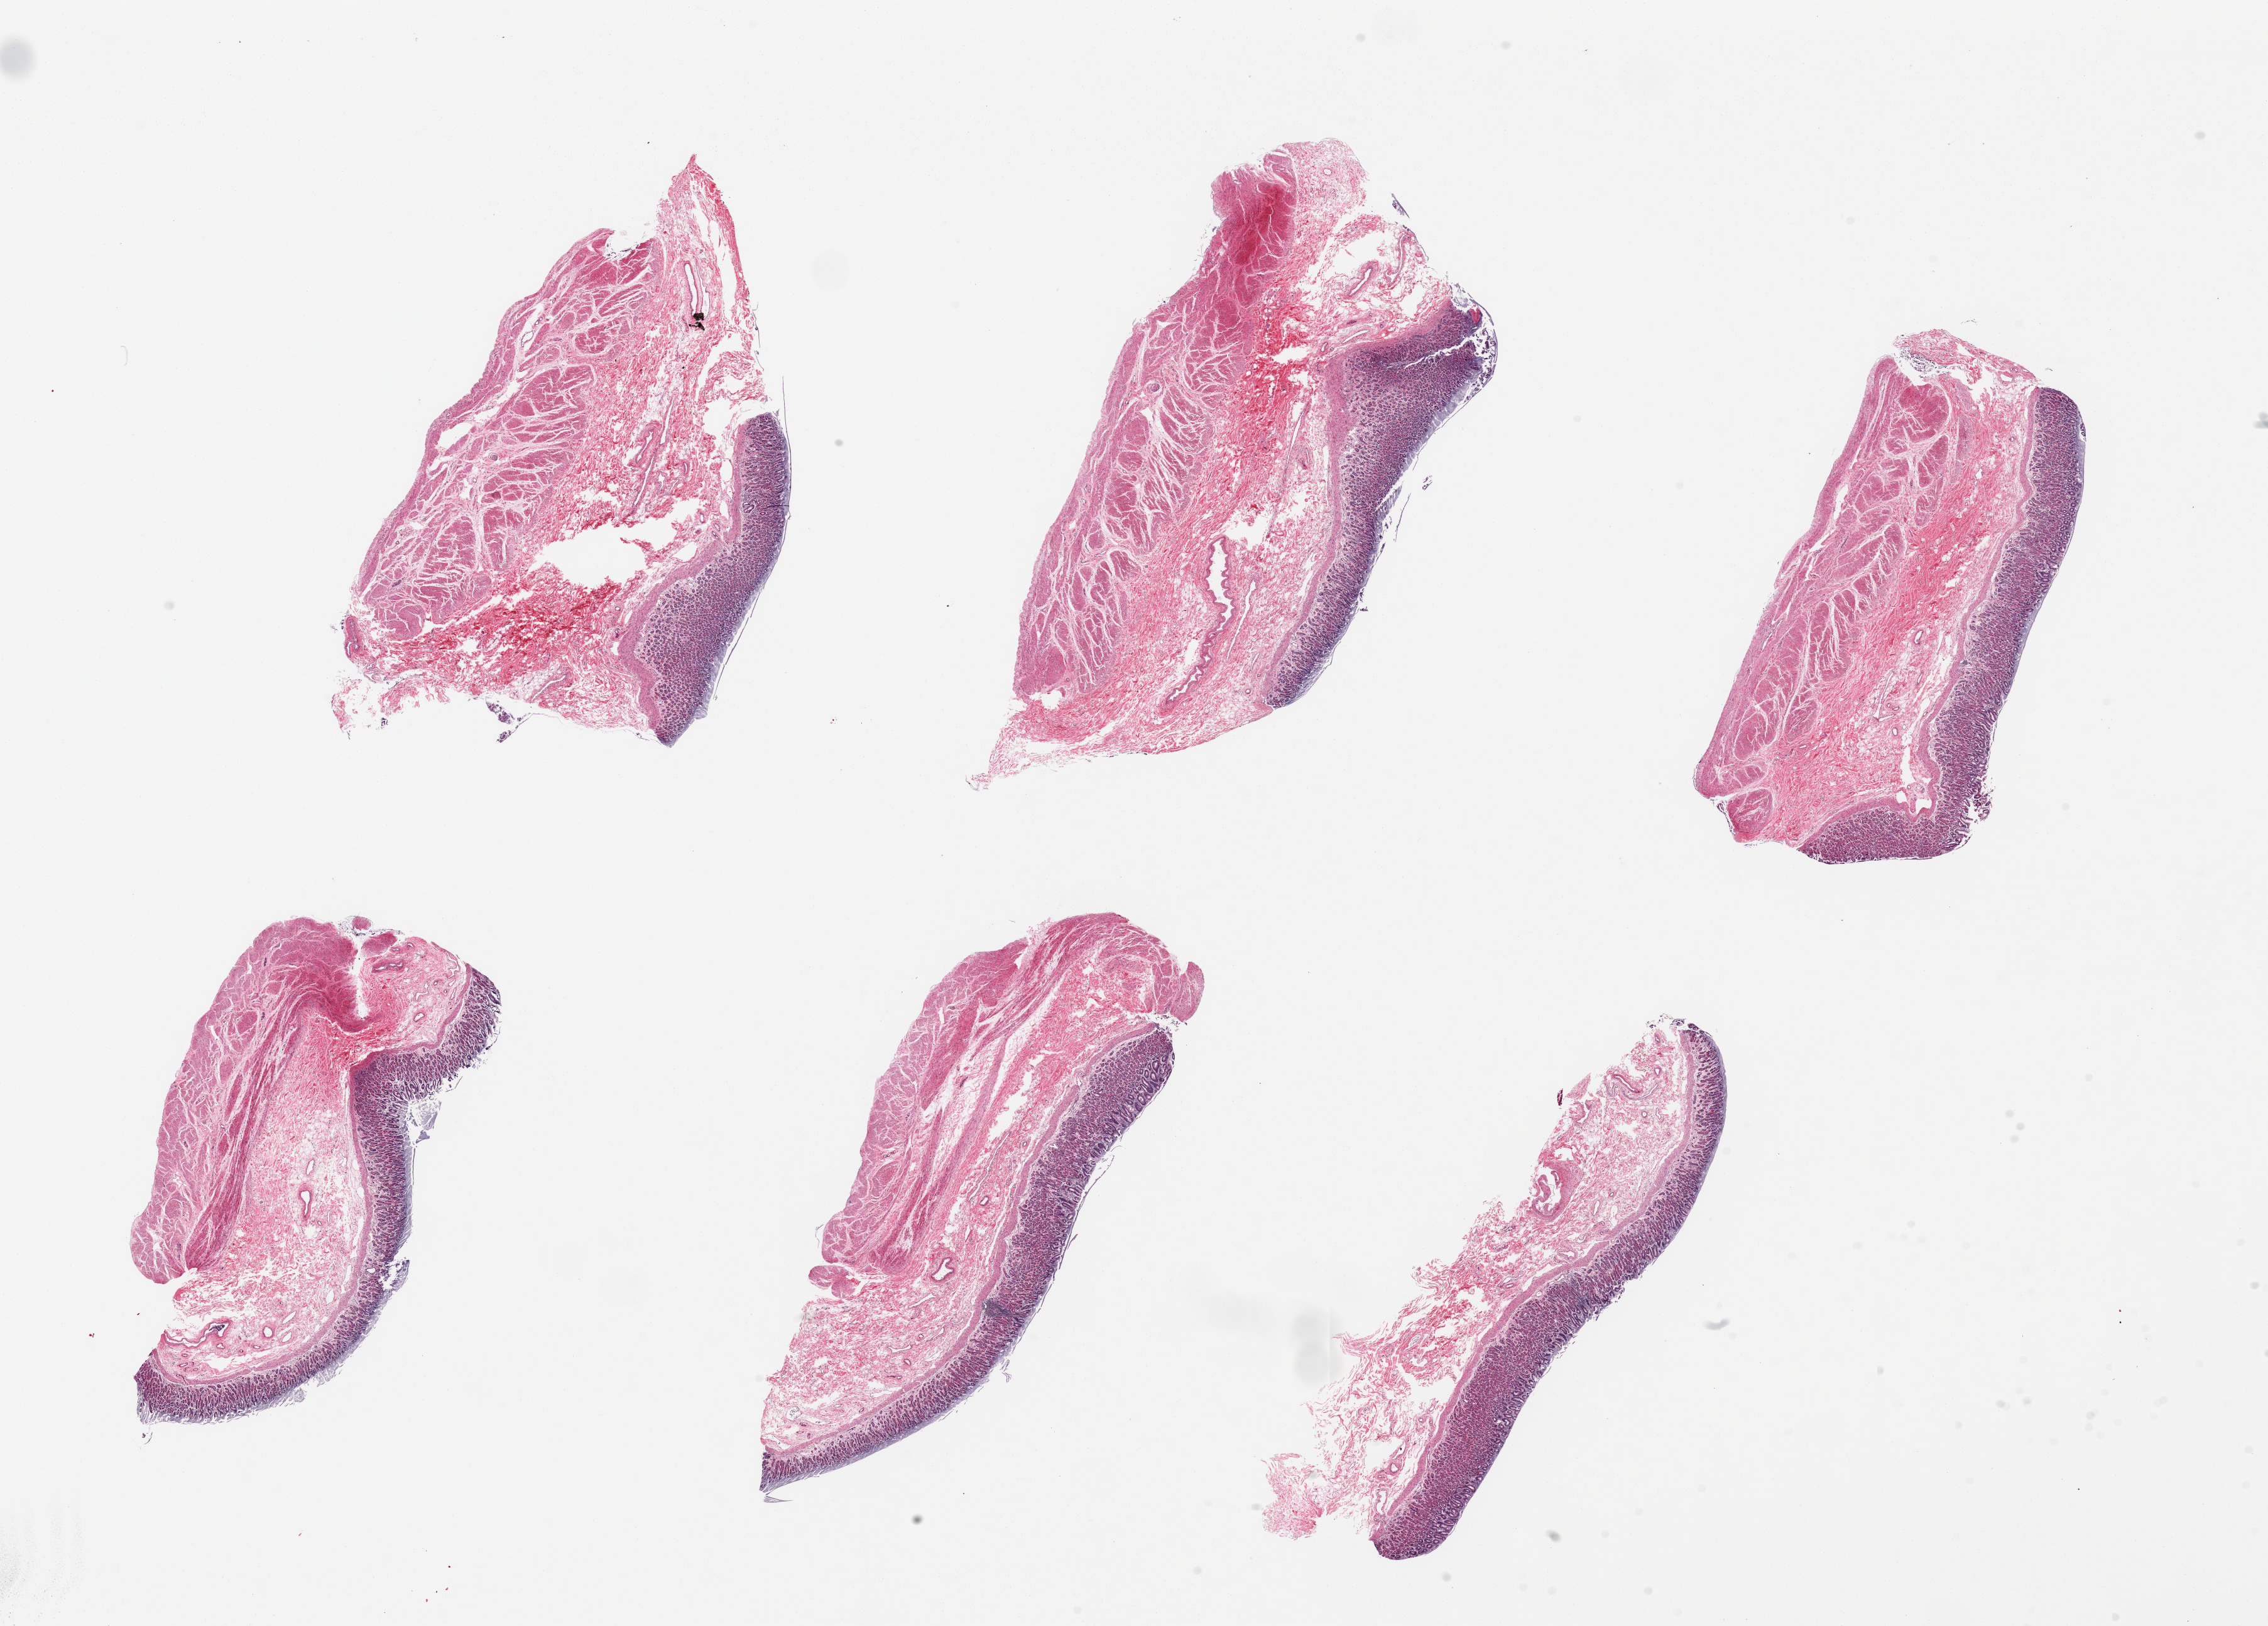
Whole-slide image, H&E stain — whole scanned area (about 28.5 x 20.5 mm, slide scanned at 20x) shown as a low-resolution overview; PAXgene-fixed, paraffin-embedded tissue; section of stomach (target tissue); donor tissue sample. Donor: female.
Pathologist's review note for this sample: 6 pieces ~7x3mm. Mucosa partly autolyzed on luminal side, ~20% of thickness.